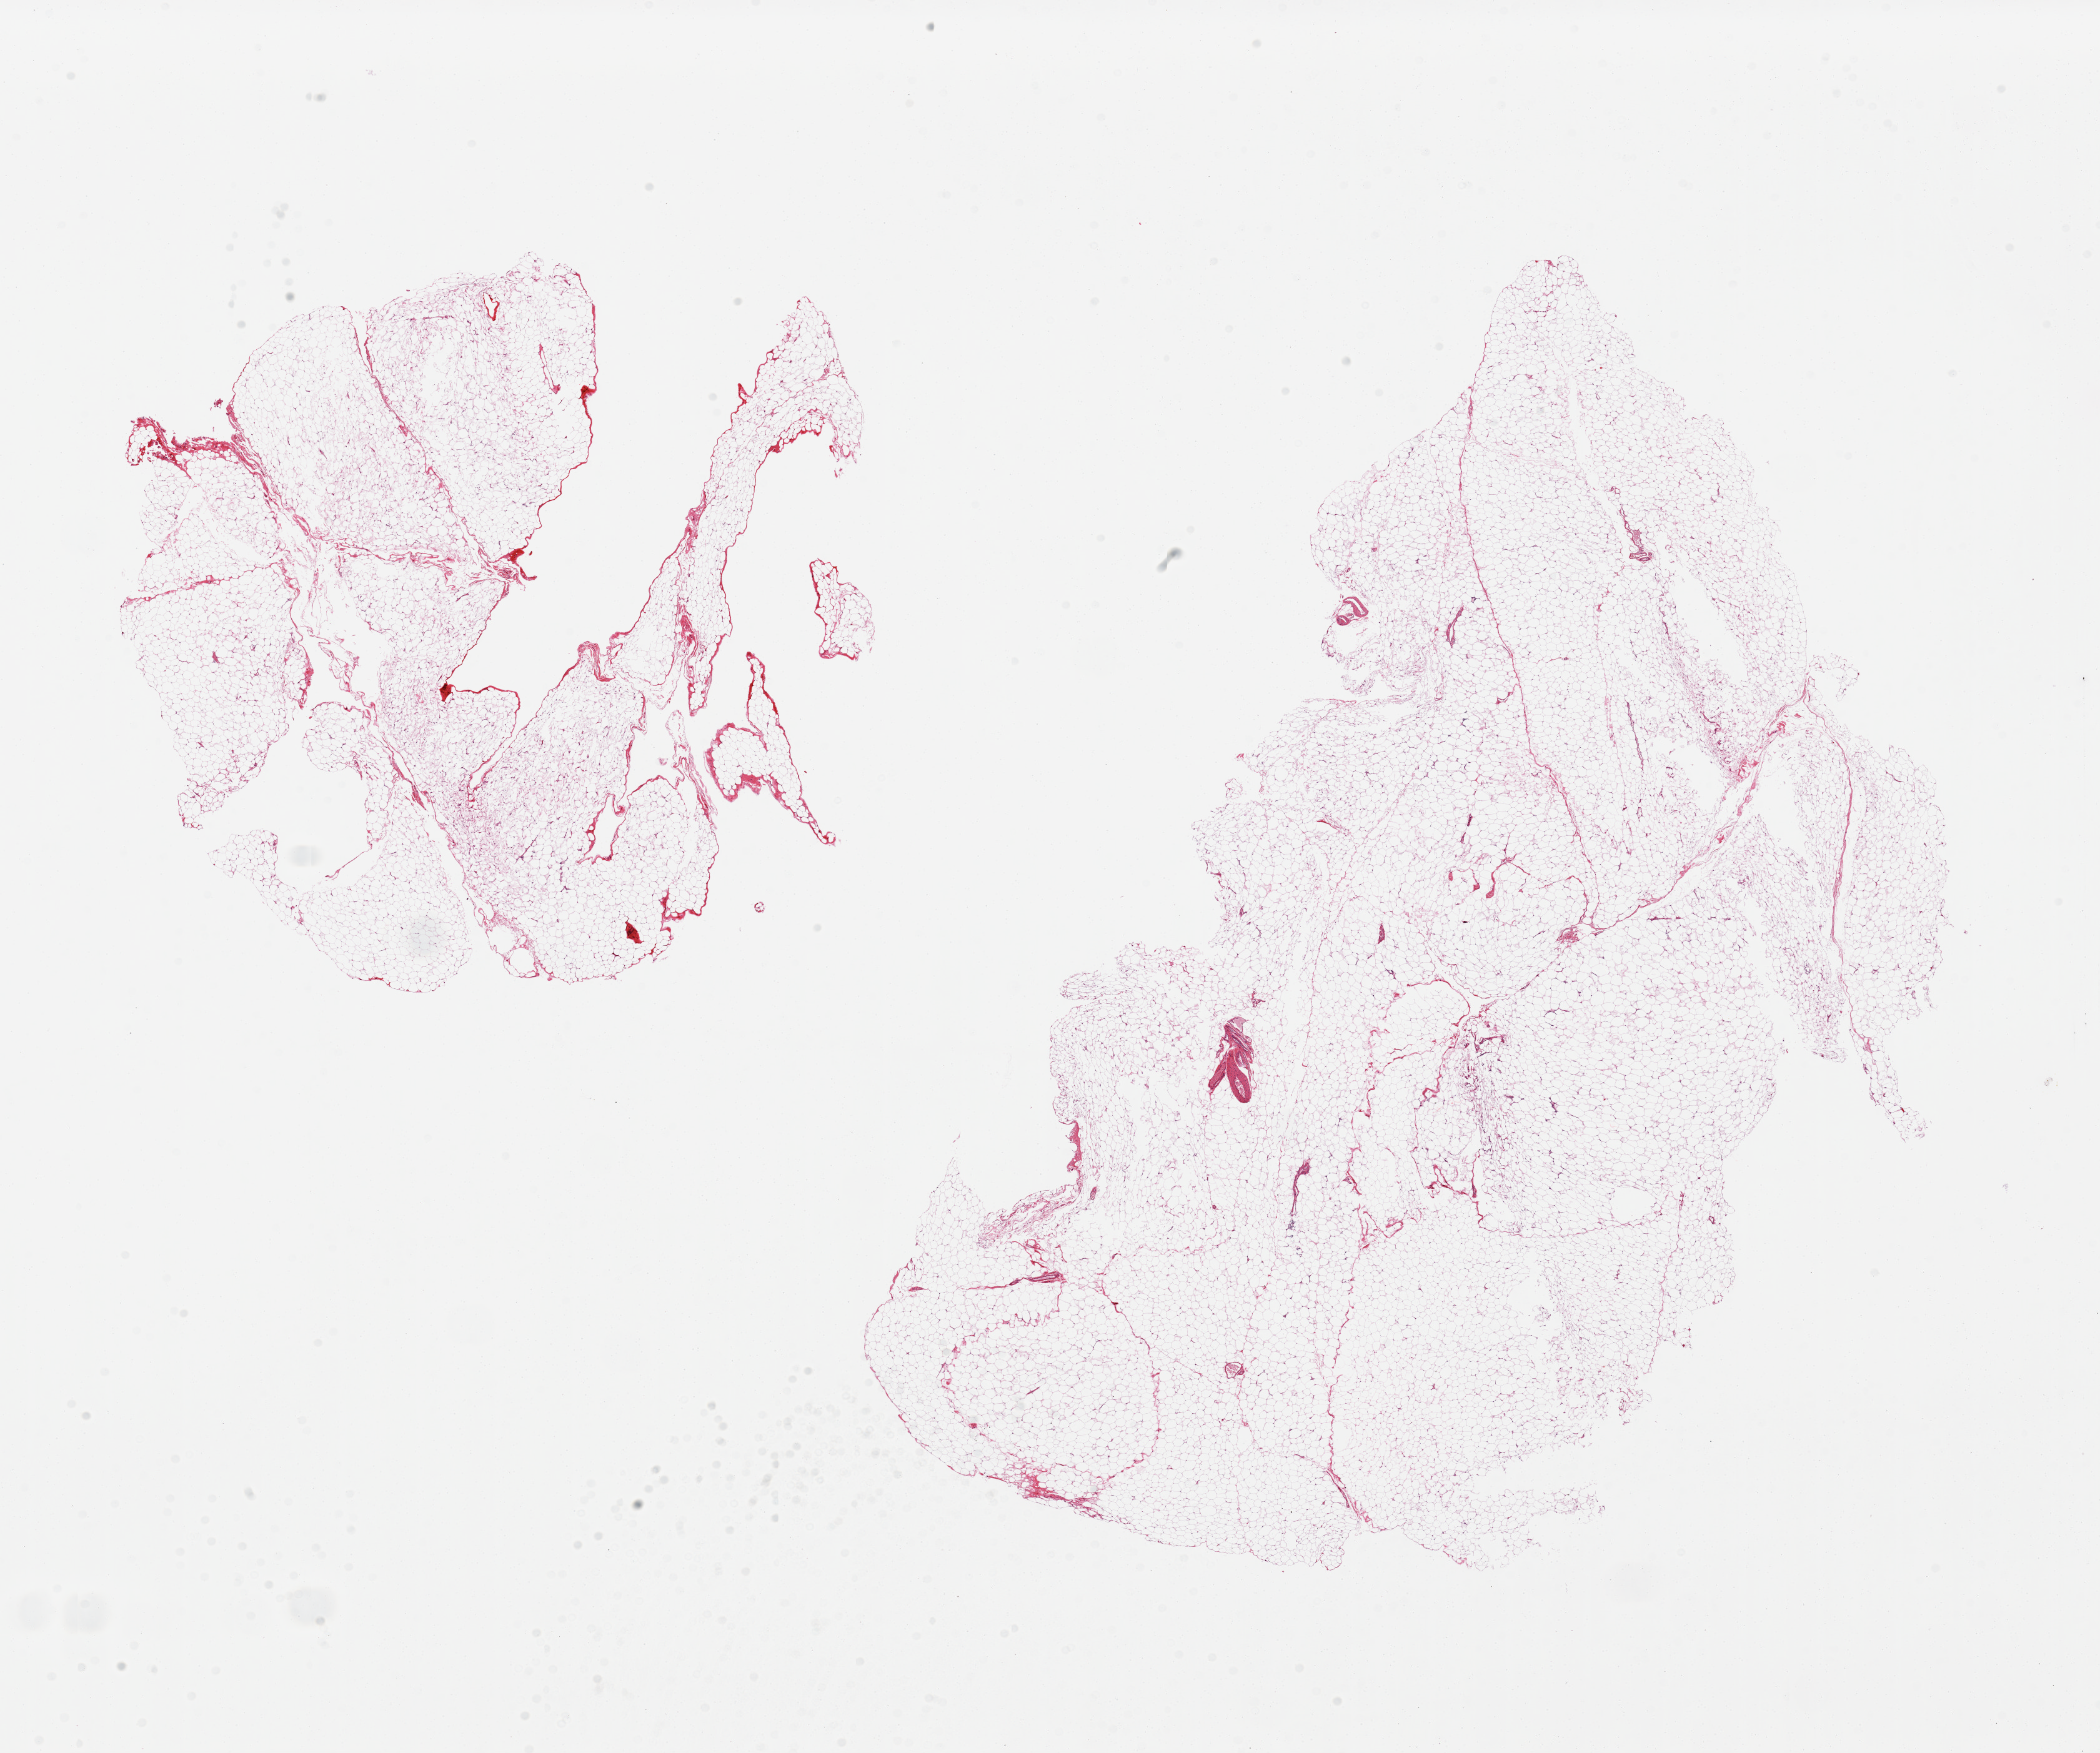
Digitized hematoxylin and eosin (H&E)-stained section, a low-resolution overview of the entire scanned area, about 26.6 x 22.2 mm (from a 20x scan), PAXgene-fixed, paraffin-embedded tissue, target tissue: omentum, tissue donor sample.
* pathologist's review note for this sample: 2 pieces